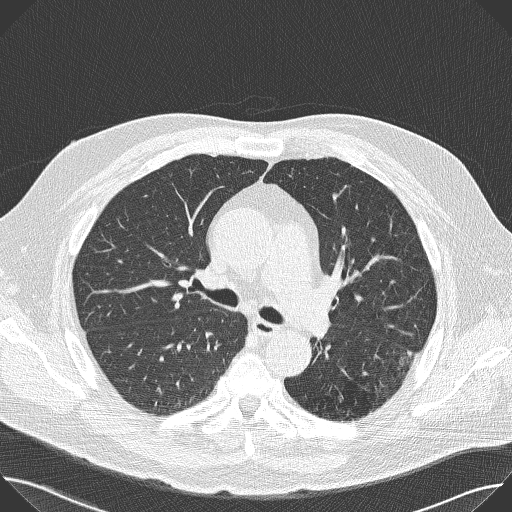
Low-dose screening chest CT, axial slice; baseline annual screen; lung window (W 1500 / L -600 HU); 2 mm slice thickness; lung (sharp) reconstruction kernel (B50f); slice 60 of 157 in the series. Male participant, aged 68 years at enrolment. Former smoker at enrolment.
Lesion marked by an expert reader, bounding box (x1, y1, x2, y2) in pixels: (367, 343, 425, 390). The screening reader recorded 2 non-calcified nodules or masses ≥4 mm on this exam; which of them this box marks is not recorded. Lung cancer was diagnosed 512 days after this screen (after the second annual screen): adenocarcinoma, NOS, left lower lobe, poorly differentiated (G3), stage IB (AJCC 6th edition), 17 mm at pathology.